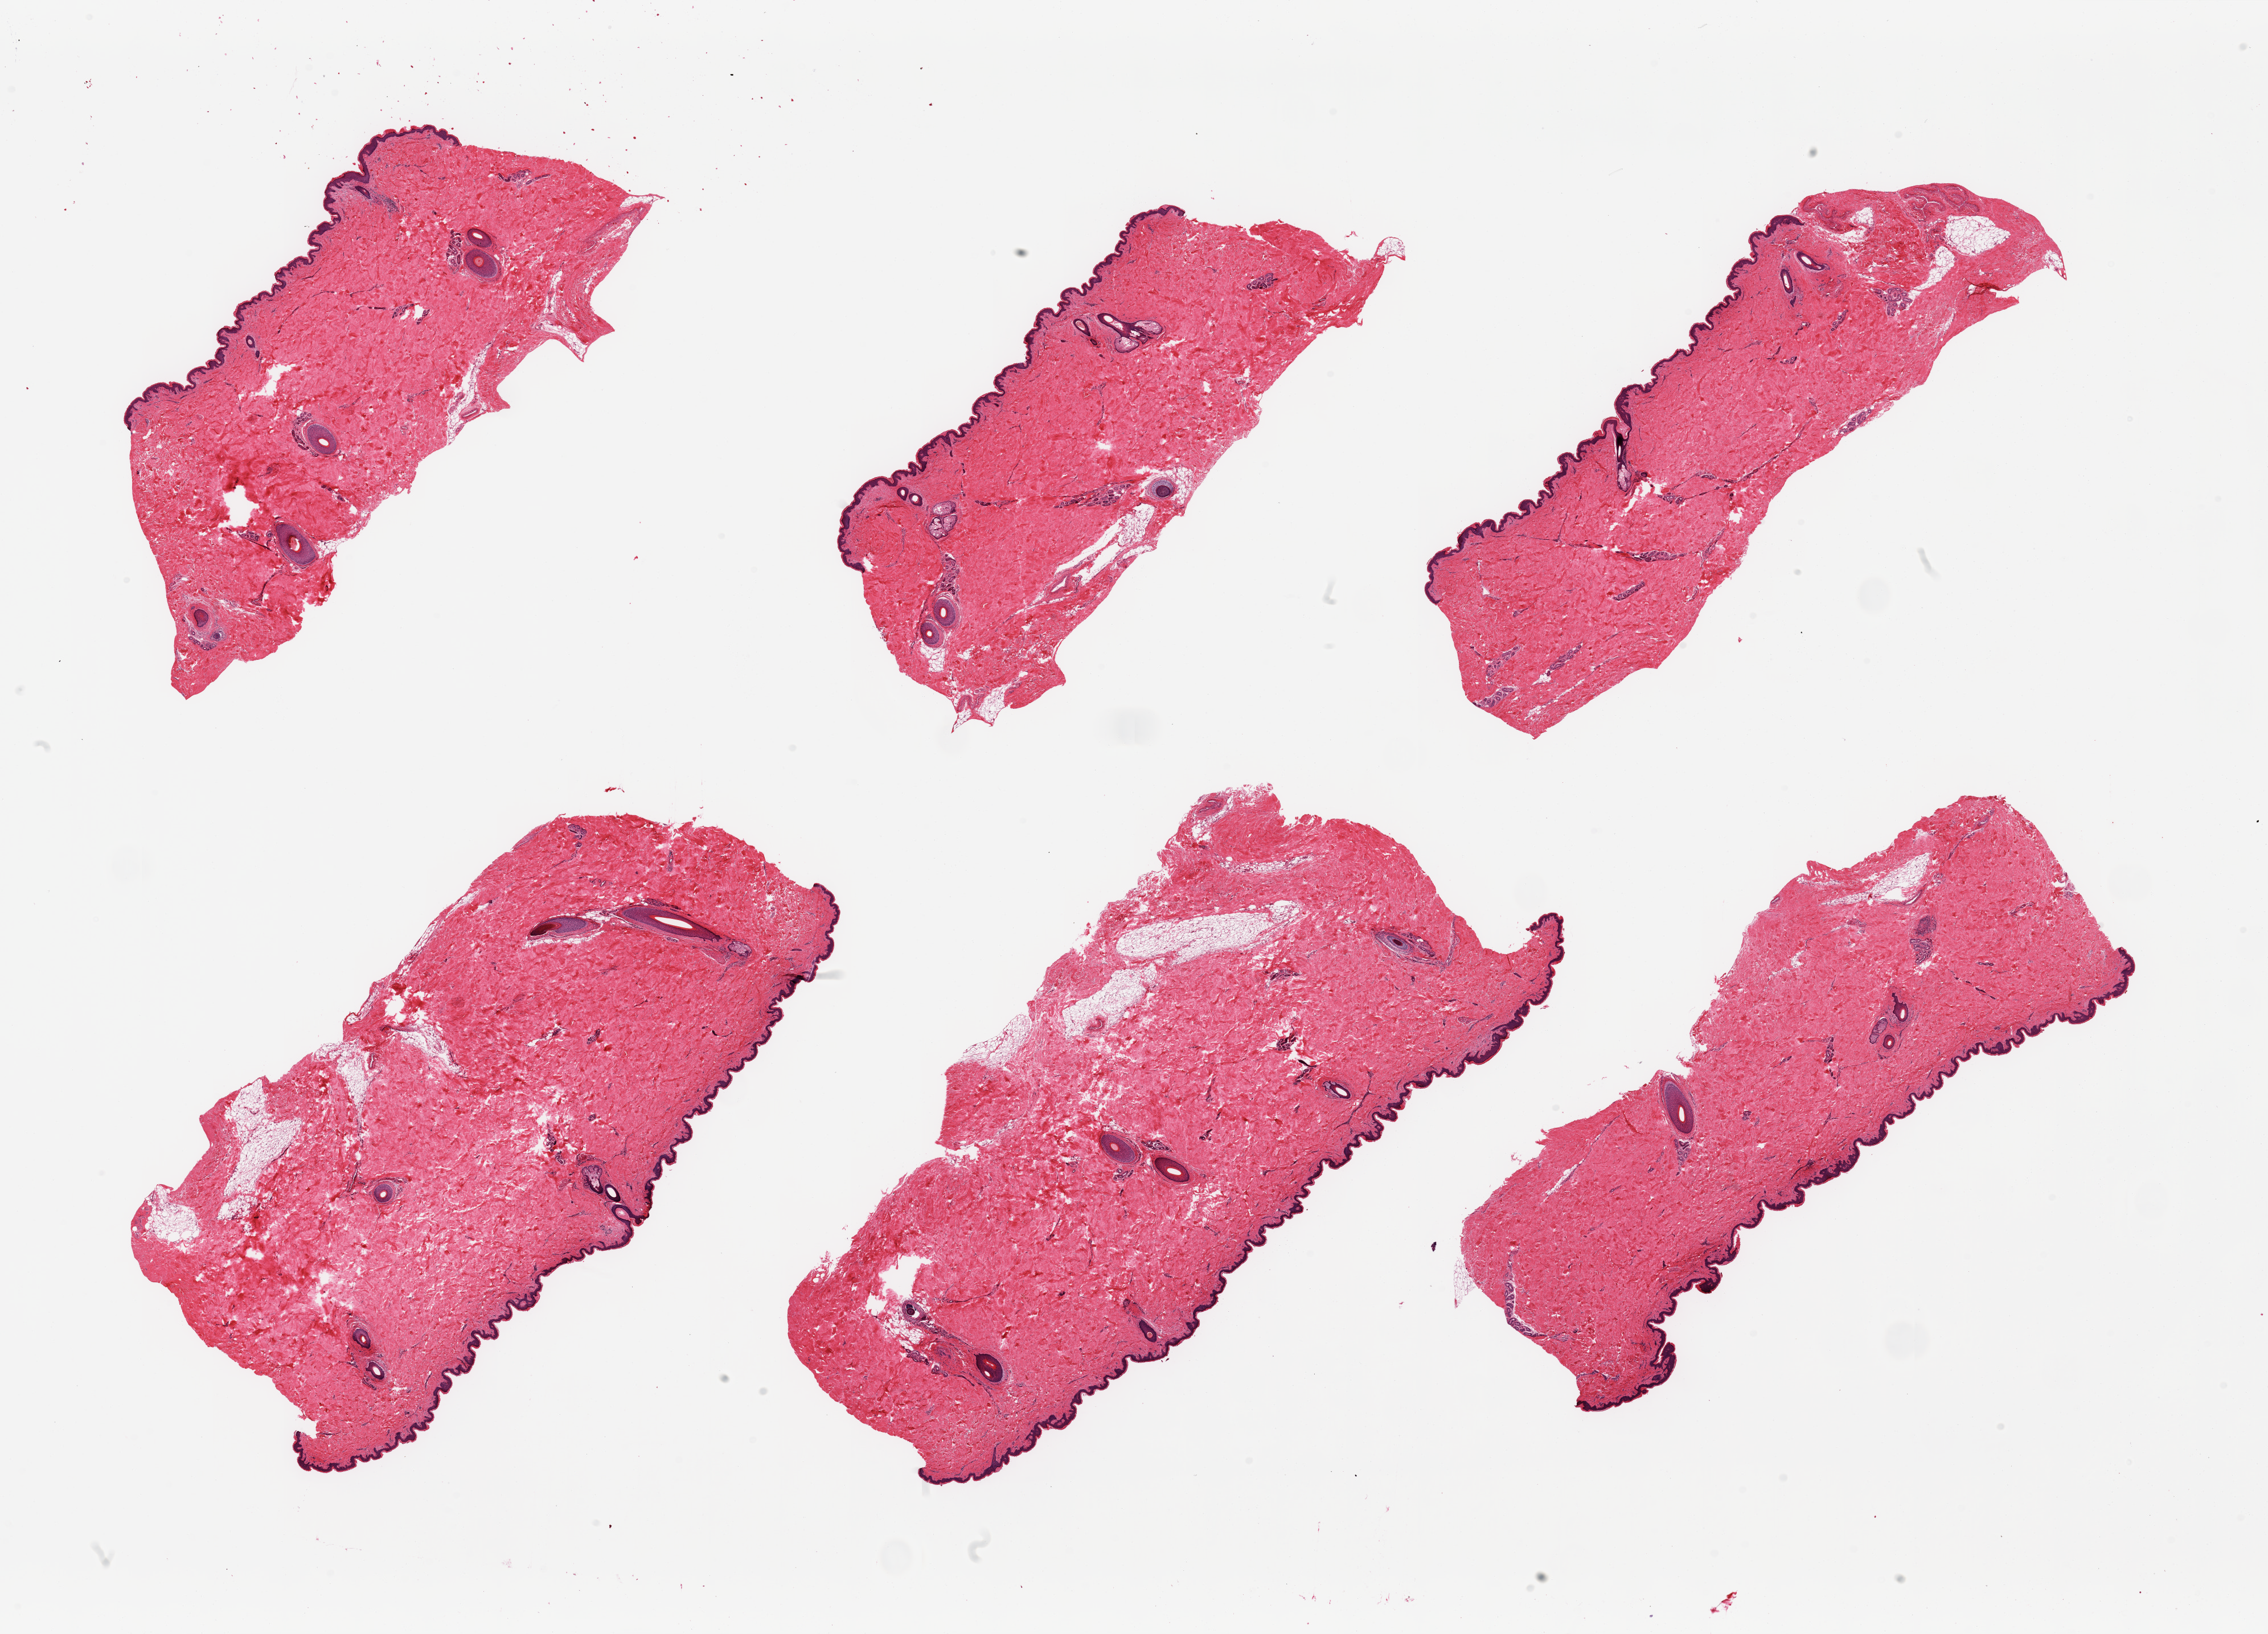
Digitized H&E-stained section — a low-resolution overview of the entire scanned area, about 31.5 x 22.7 mm; PAXgene-fixed, paraffin-embedded tissue; sampled site (target tissue): skin of suprapubic region; donor tissue sample. Donor sex: male.
* review note (as recorded): 6 pieces; well trimmed; up to 10% dermal fat; up to 4 hair follicles per piece